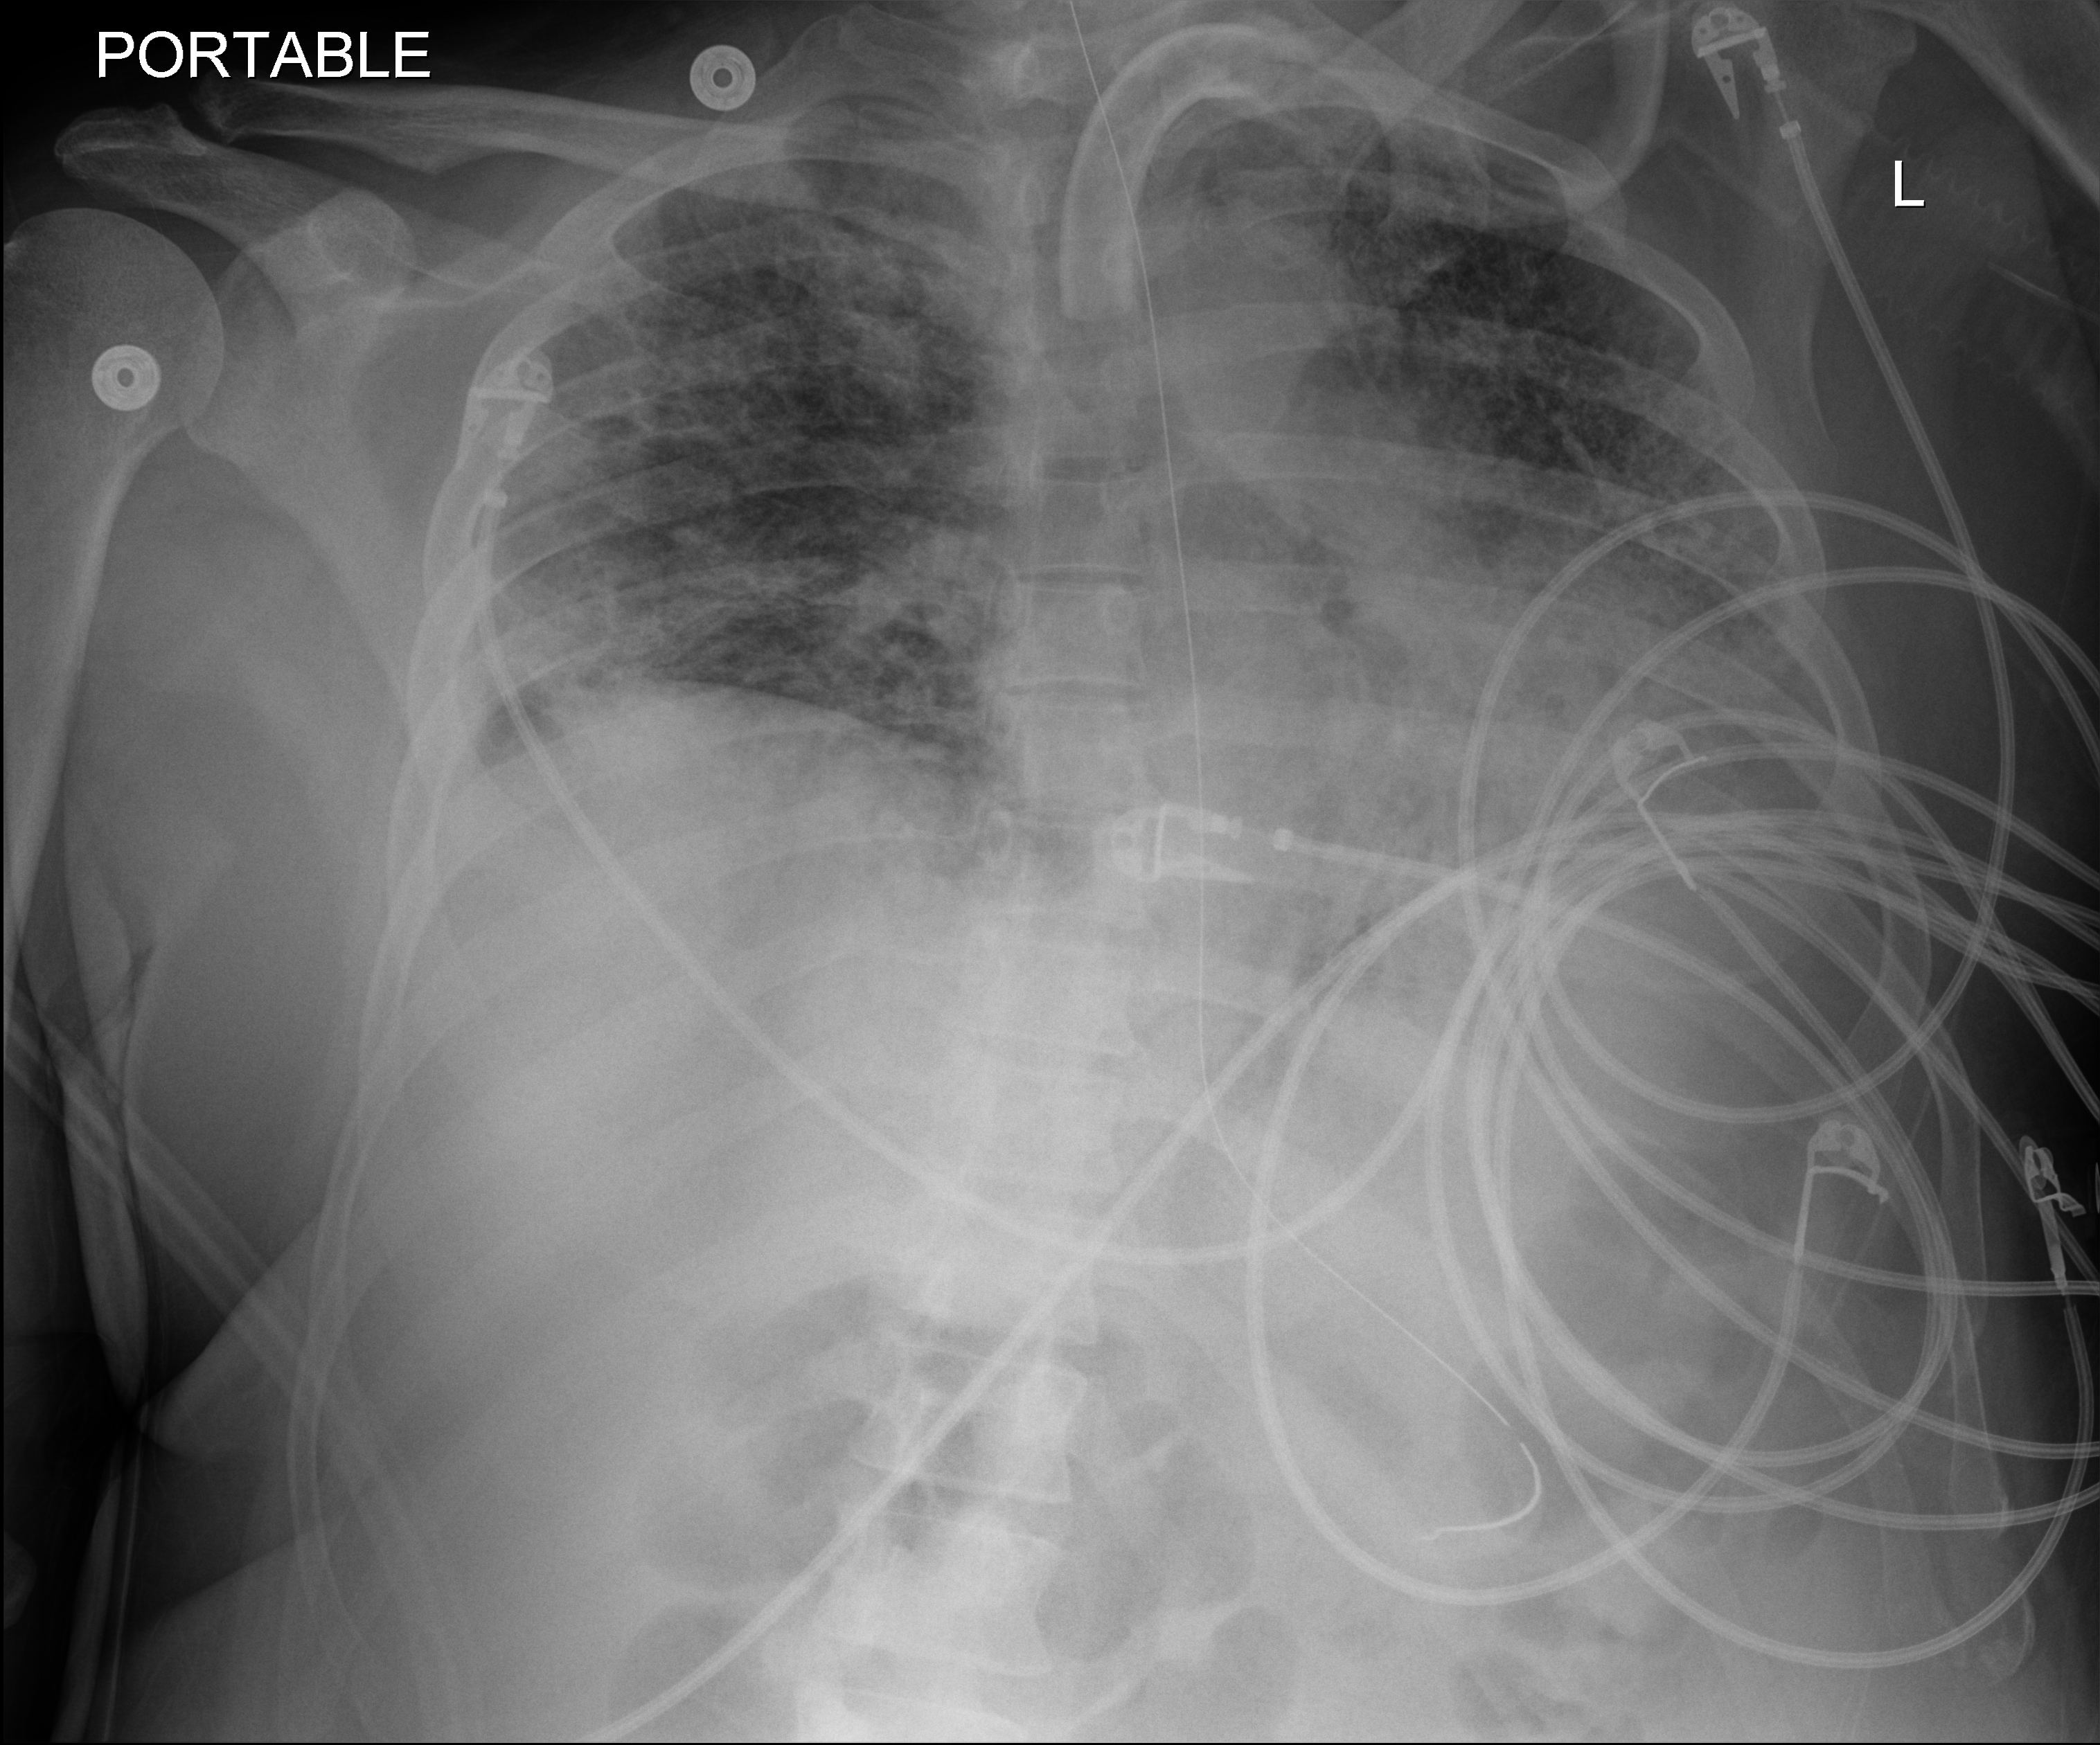
Bedside chest radiograph (digital radiography). Male patient hospitalised with COVID-19, age 18–59 years.
Hospital-stay facts (about this admission, not read from this image; timing relative to this image not recorded): admitted to intensive care during this hospital stay: yes.